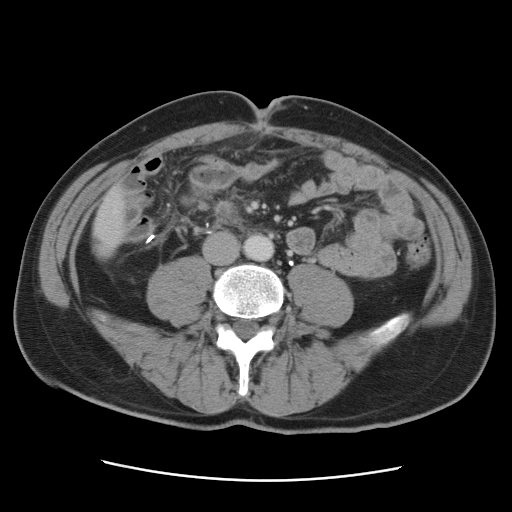
Contrast-enhanced abdominal CT, one axial slice. Slice 6 of 89 in the series (ordered by position). 120 kVp. Intravenous contrast given. Soft-tissue window (W 400 / L 40 HU). 512 × 512 image matrix. Male patient, age 59 years. Case-level facts recorded for this patient, not image findings: diagnosis: colorectal cancer liver metastases, imaged before liver resection.
Structures marked on this image (outlined manually by an expert reader):
- liver: bounding box (x1, y1, x2, y2) in pixels: (94, 191, 125, 260)
- planned liver remnant (the part of the liver to remain after resection): (94, 191, 126, 259)